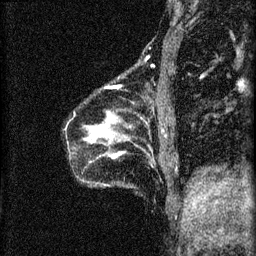
Breast MRI (dynamic contrast-enhanced), one sagittal slice; slice 10 of 60 in the series (ordered by position); 3 images stored at this slice position (order not interpretable as contrast timing); 1.5 T; TE 4.2 ms, TR 8.2 ms; 2 mm slice thickness; 256 × 256 image matrix, field of view 180 × 180 mm. Female patient, age 40 years.
Structures marked on this image (semi-automatic segmentation, software-assisted and operator-edited):
- analysis volume of interest (the breast-tissue region the enhancement analysis was run in; not a lesion): bounding box <84,88,171,165> (left, top, right, bottom; pixels)
- tumour enhancement mask (voxels above the 70 % enhancement threshold inside the analysis volume of interest): <92,126,121,159>